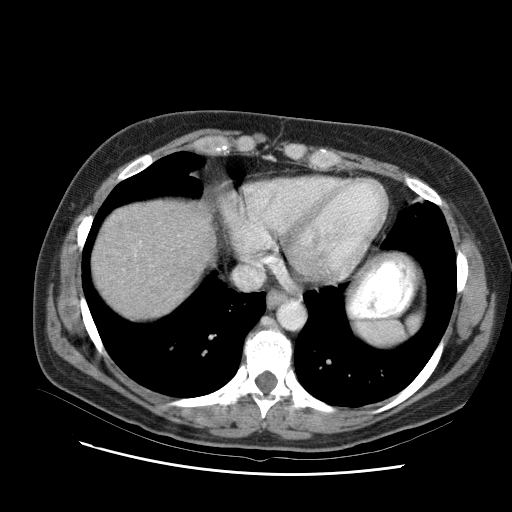
Contrast-enhanced abdominal CT (liver protocol), one axial slice. Position 86 of 95 along the scan axis. Reconstruction kernel STANDARD. One of 2 acquisitions stored at this slice position. Soft-tissue window (W 400 / L 40 HU). 2.5 mm slice thickness. 512 × 512 image matrix, field of view 360 × 360 mm. From the clinical record (not read from this slice): diagnosis: hepatocellular carcinoma (patient treated with transarterial chemoembolisation; whether this scan precedes or follows treatment is not stated here); TNM stage (as recorded): Stage-I; Child-Pugh class: B.
Annotated regions visible in this slice (semi-automatic segmentation, software-assisted and operator-edited):
- liver parenchyma outside the tumour (the mass and vessels are separate outlines, so this box may not span the whole liver): box from (x=104, y=210) to (x=192, y=290) px